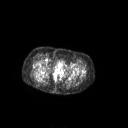
FDG PET of an extremity soft-tissue mass (from a PET/CT study), one axial slice. Slice 61 of 267 in the series (ordered by position). 3.27 mm slice thickness. 128 × 128 image matrix. Patient: female, 70 years. From the clinical record (not read from this slice): histological type: synovial sarcoma; grade: intermediate; site of the primary tumour: right buttock.
Annotated regions visible in this slice (expert contour drawn on MRI and transferred to this co-registered scan by the dataset authors):
- gross tumour volume including surrounding oedema: bounding box [x1, y1, x2, y2] px = [33, 69, 46, 80]
- gross tumour volume (mass): [35, 69, 41, 74]